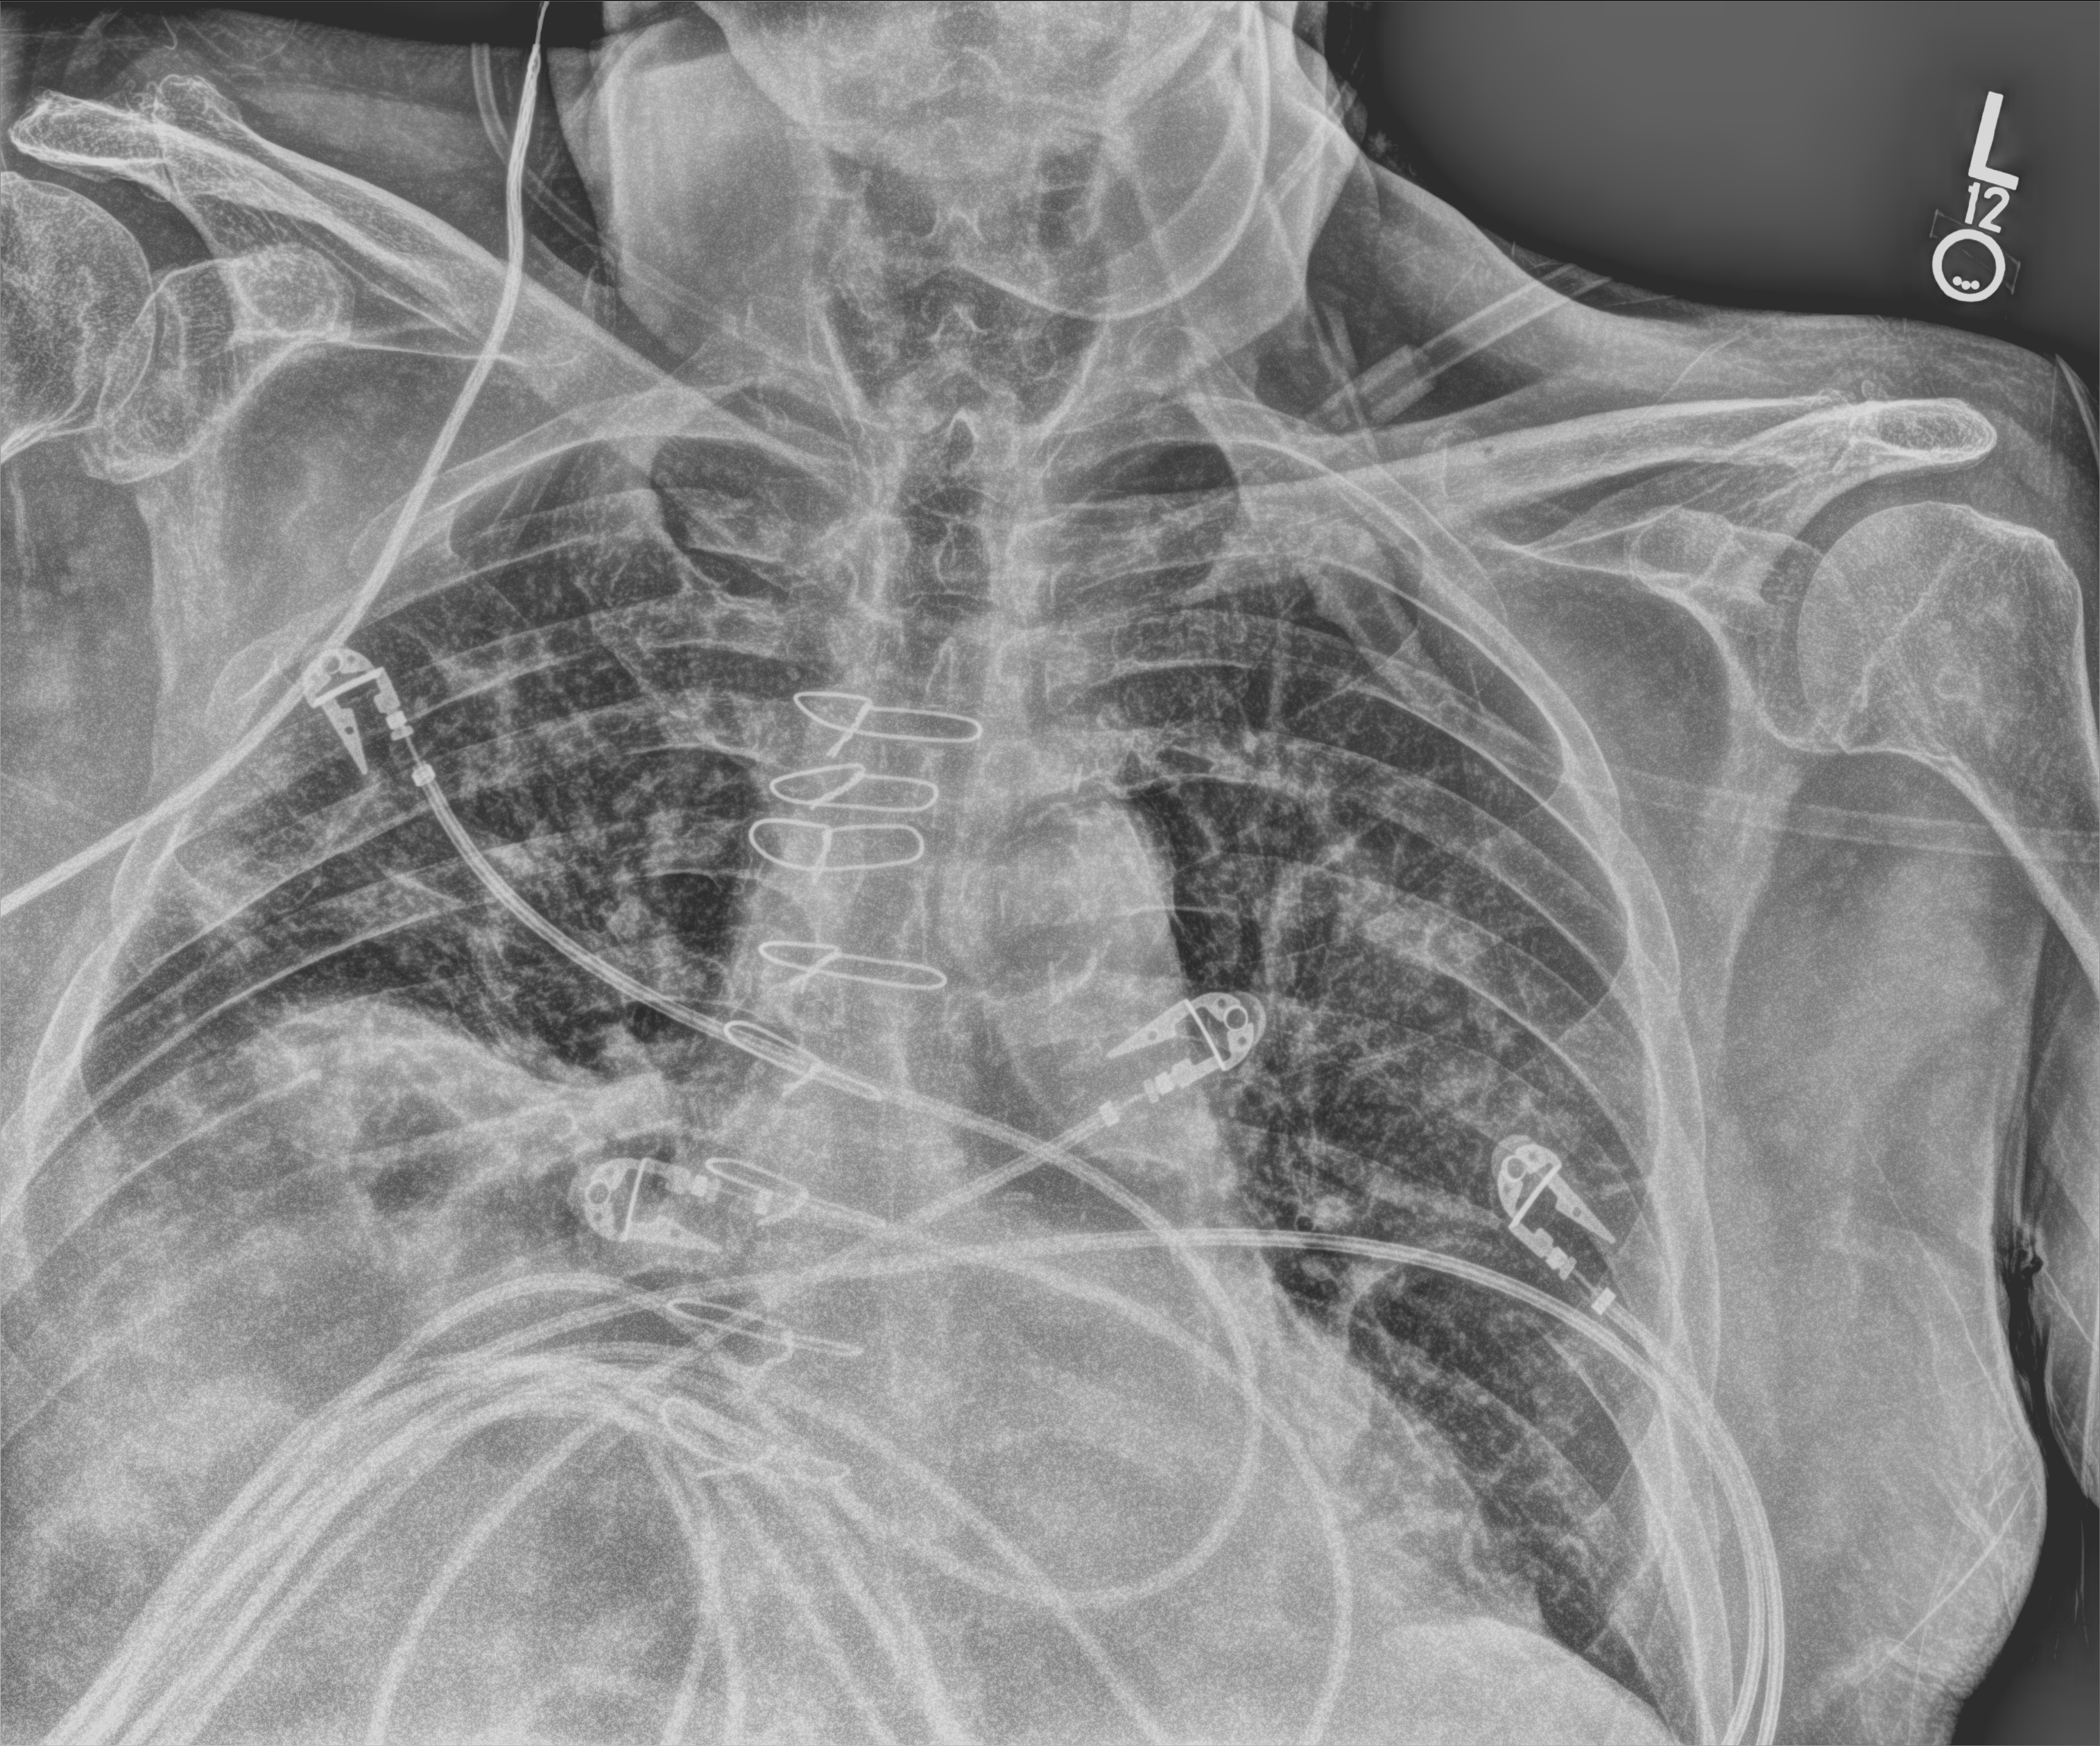
Bedside chest radiograph (computed radiography); anteroposterior (AP) projection. Male patient hospitalised with COVID-19, age 75–90 years.
From the hospital-stay record, not from the radiograph (when in the stay this image was taken is not recorded):
- mechanically ventilated during this hospital stay: no